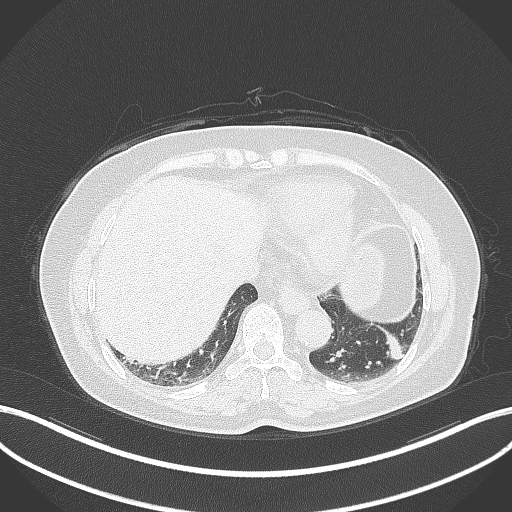
Chest CT, one axial slice; slice 101 of 311 in the series (ordered by position); 120 kVp; lung window (W 1500 / L -600 HU); 1 mm slice thickness; 512 × 512 image matrix, field of view 400 × 400 mm. Patient: female, 59 years. From the clinical record (not read from this slice): clinical TNM (as recorded): T2a N0 M0; histopathological grade: G2-3.
Structures marked on this image (bounding box drawn by a radiologist):
- lung tumour (recorded histology: adenocarcinoma): bounding box (x1, y1, x2, y2) in pixels: (379, 323, 406, 364)